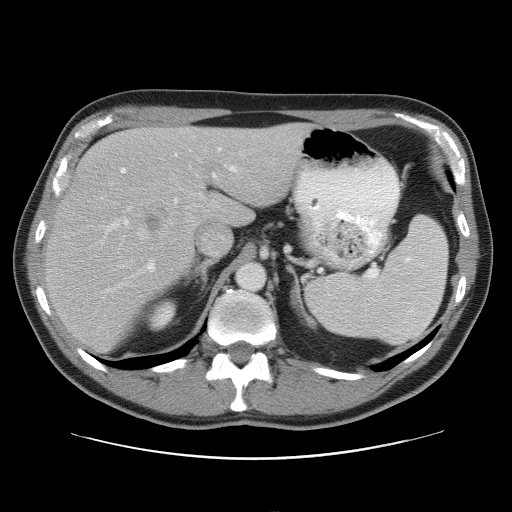
Contrast-enhanced abdominal CT, one axial slice; slice 39 of 52 in the series (ordered by position); reconstruction kernel STANDARD; 120 kVp; soft-tissue window (W 400 / L 40 HU); 512 × 512 image matrix. Male patient, age 70 years. From the clinical record (not read from this slice): diagnosis: colorectal cancer liver metastases, imaged before liver resection; multiple liver metastases: yes; largest metastasis: 4 cm; disease in both lobes: yes.
Outlined on this slice (manually delineated by an expert):
- hepatic veins: bounding box (x1, y1, x2, y2) in pixels: (137, 150, 244, 239)
- liver: (46, 124, 307, 354)
- planned liver remnant (the part of the liver to remain after resection): (108, 124, 307, 212)
- portal vein (with intrahepatic branches): (105, 147, 238, 293)
- liver metastasis: (145, 210, 168, 233)